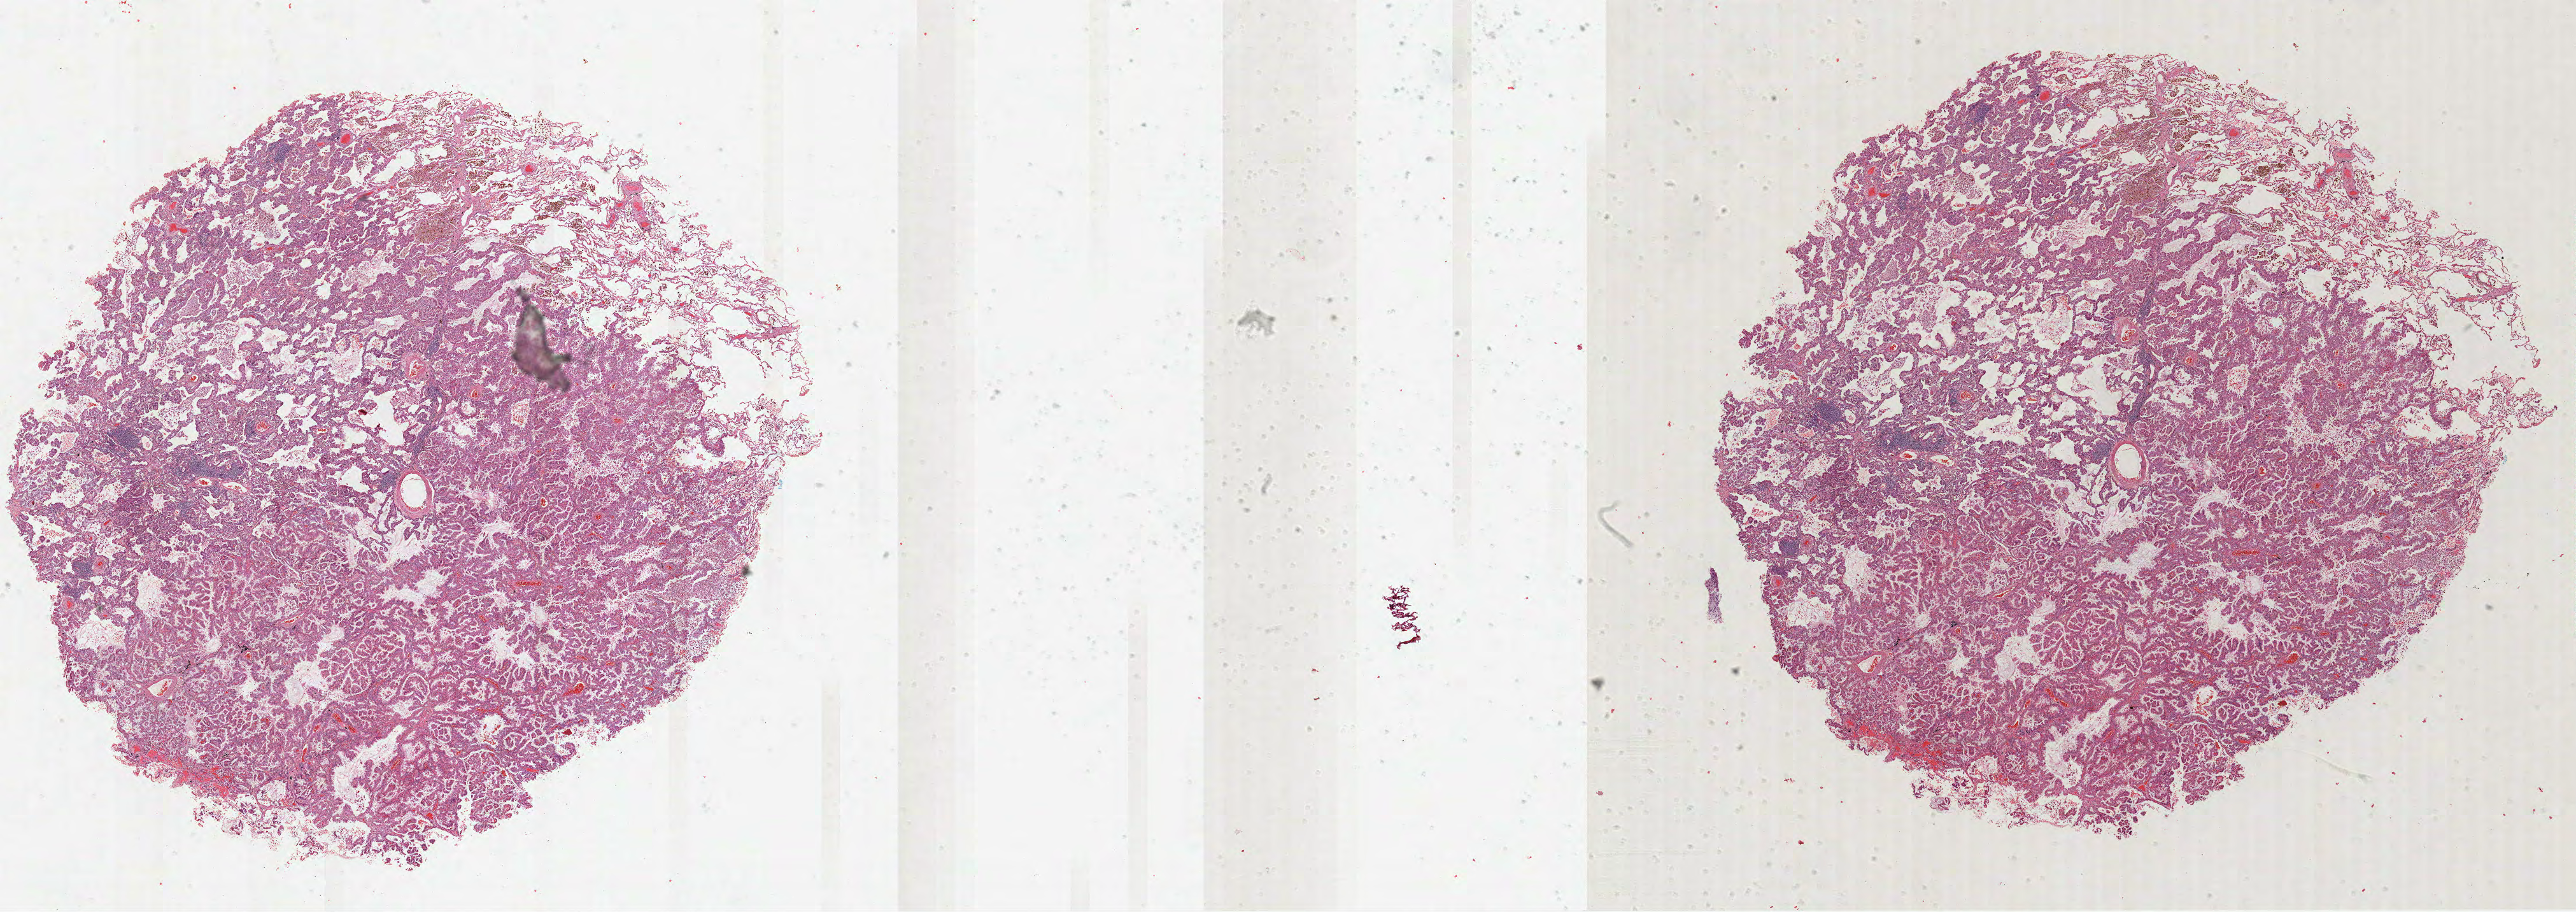
Whole-slide histology image, Hematoxylin and eosin (H&E) stained, a low-resolution overview of the entire scanned area, about 32.6 x 11.5 mm; formalin-fixed paraffin-embedded (FFPE) diagnostic section; lung, primary tumour sample. Female patient; age at initial diagnosis 60 years.
* diagnosis: Adenocarcinoma, NOS (upper lobe, lung)
* AJCC pathologic stage: IA (6th edition)